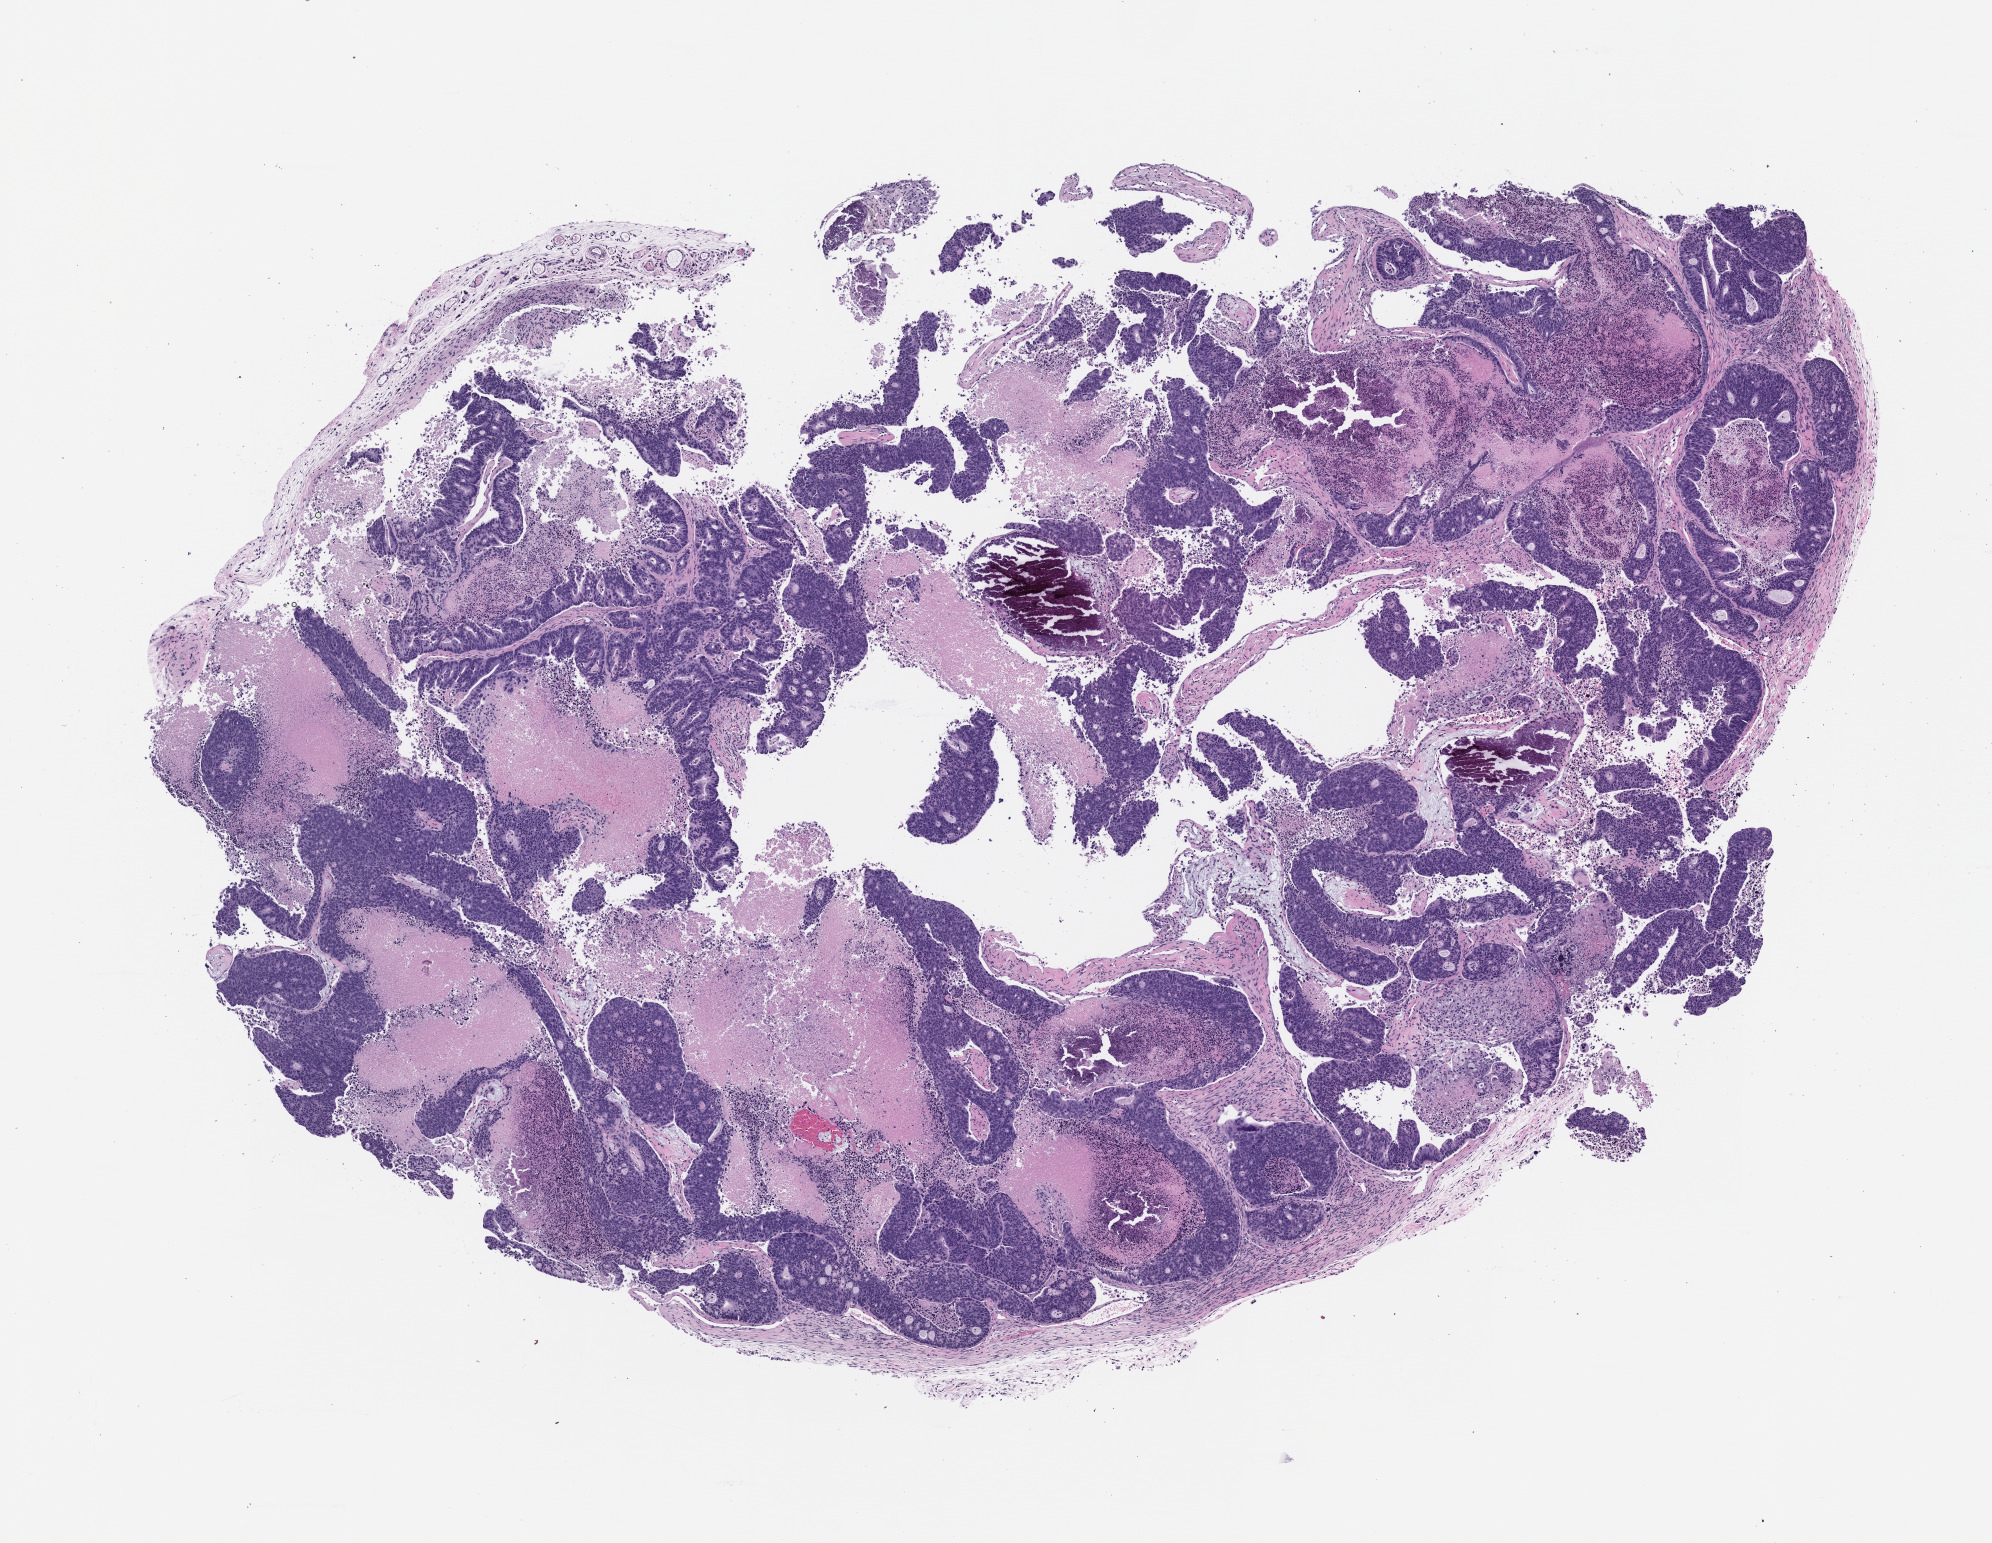
Whole-slide image, haematoxylin and eosin: patient-derived xenograft (human tumor grown in a mouse), passage 1 — whole scanned area (about 8.0 x 6.2 mm) shown as a low-resolution overview; formalin-fixed paraffin-embedded section; originating tumor site category: colon.
Originating patient diagnosis: Colon Adenocarcinoma.